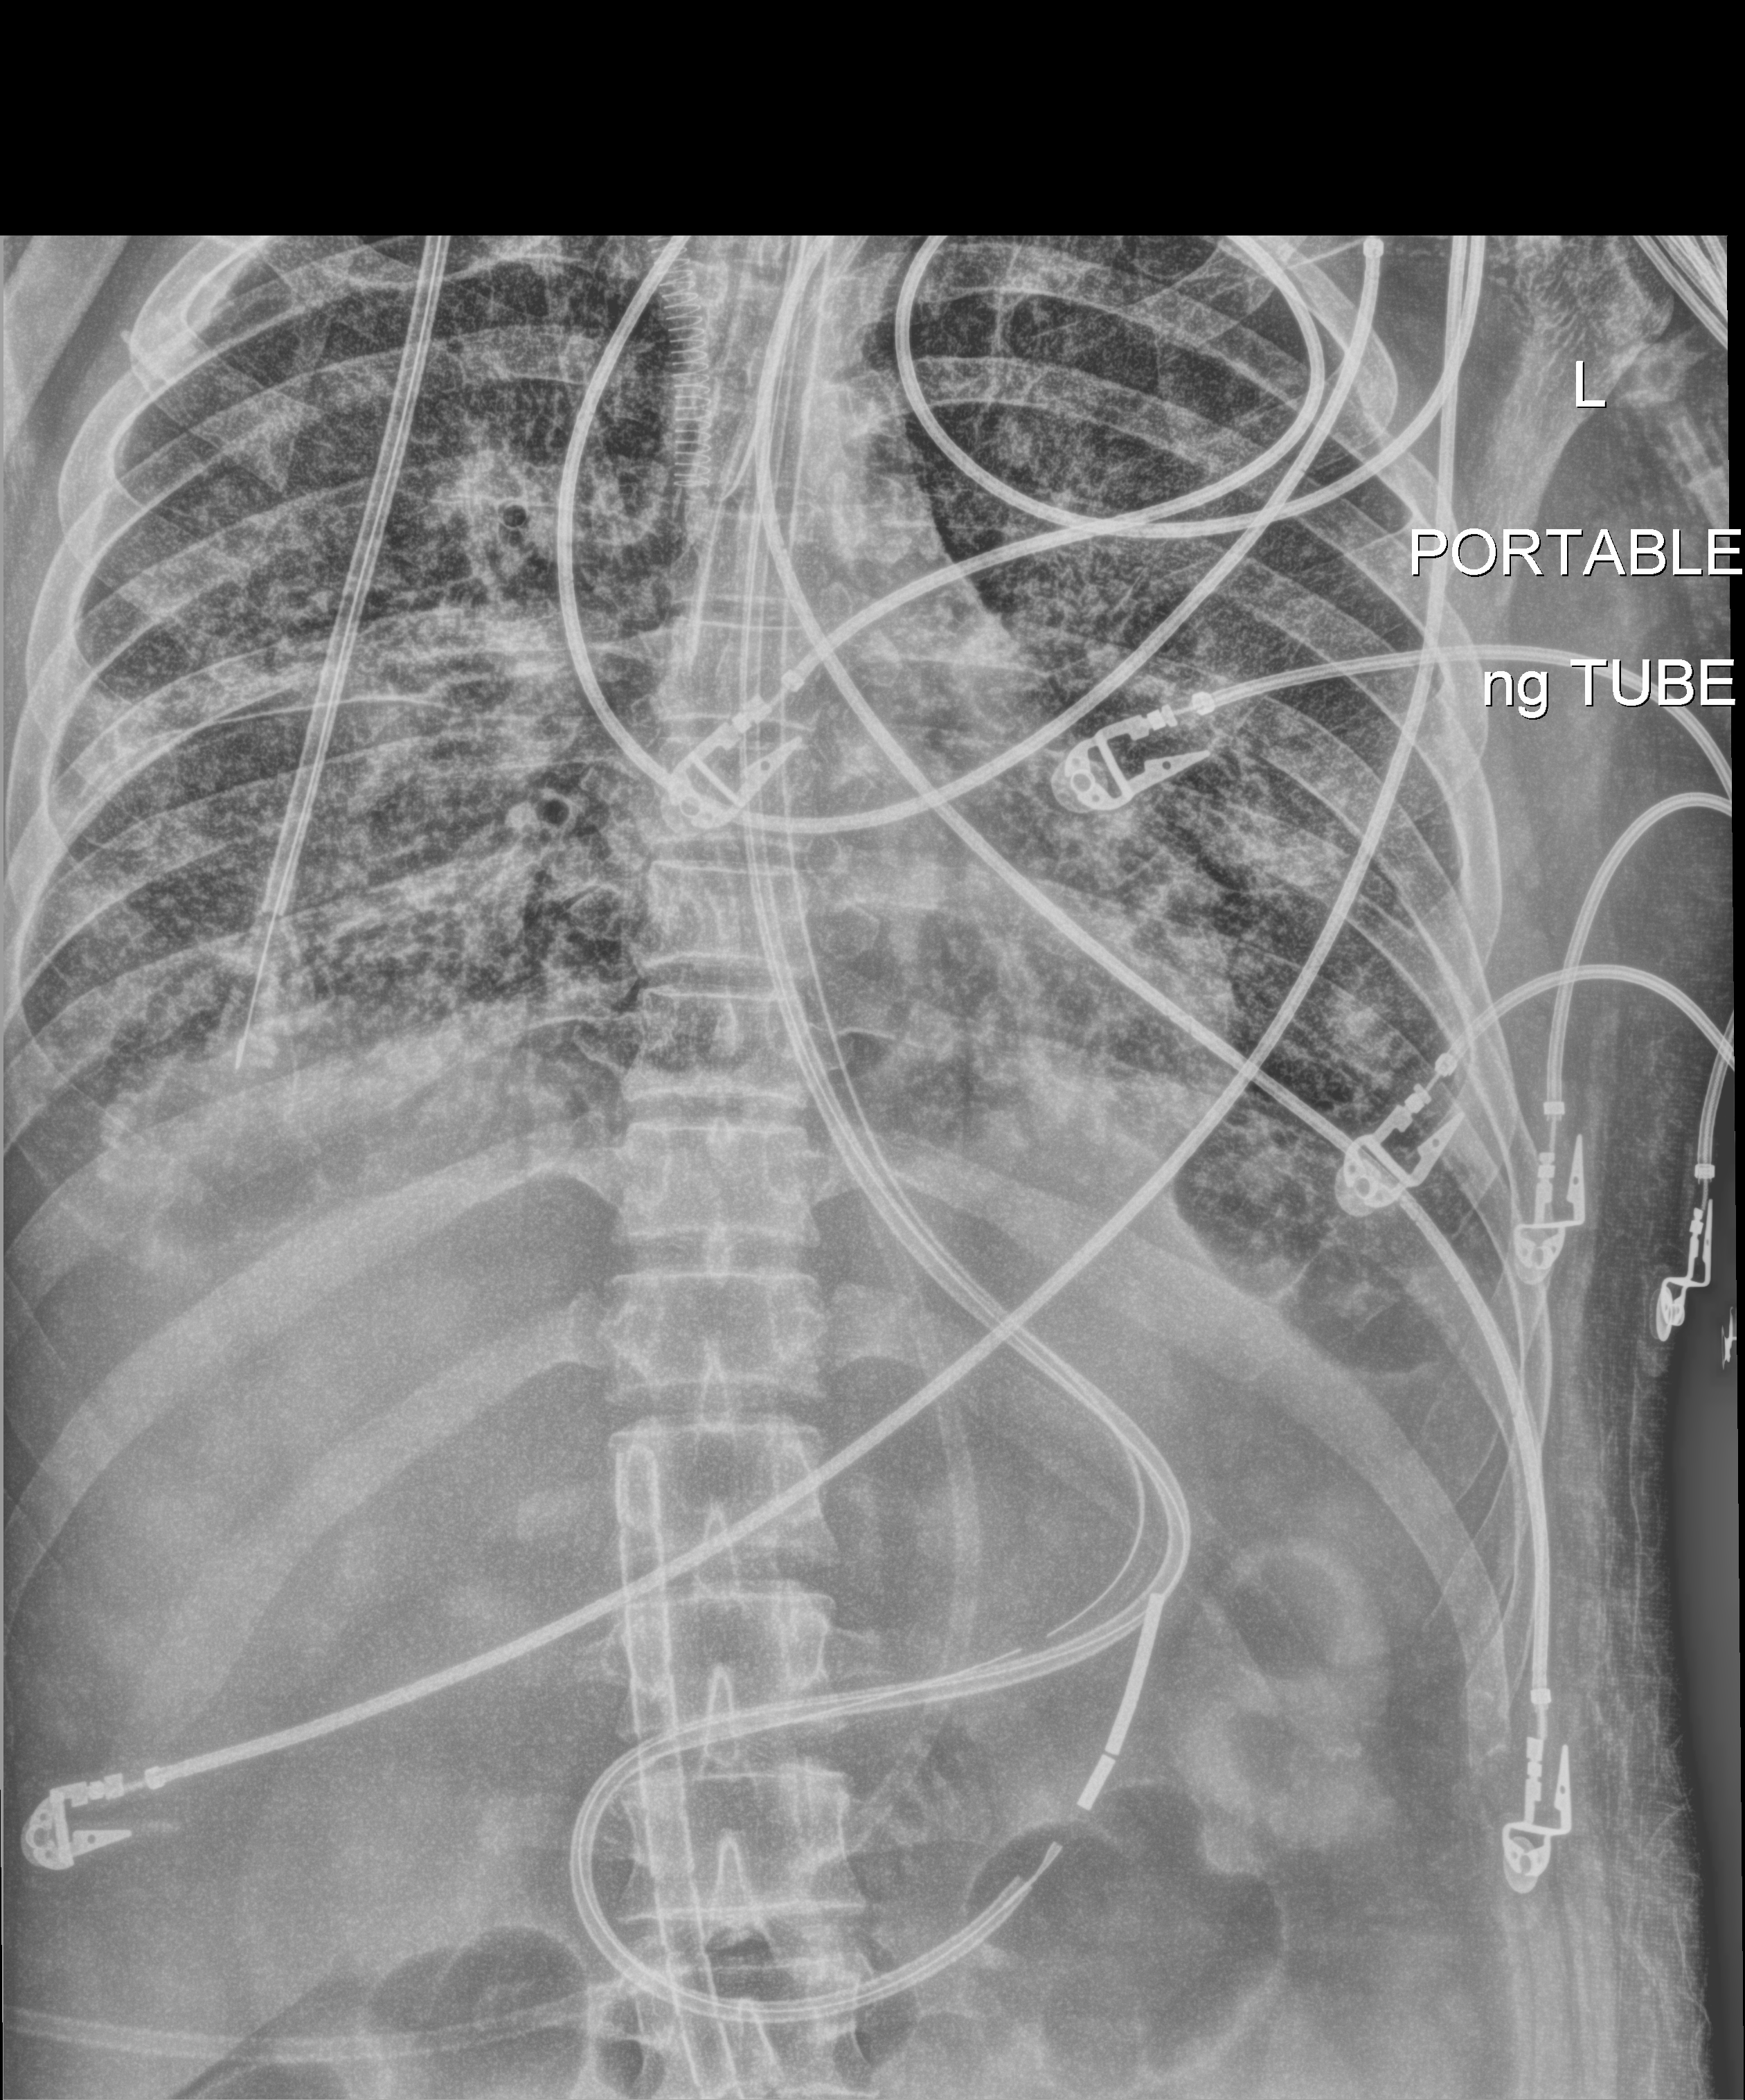
Portable abdomen radiograph; anteroposterior (AP) projection. Patient hospitalised with COVID-19, aged 18–59 years.
Admission-level facts for this patient (not findings on this image; timing relative to this image not recorded): smoking status (admission record): never; admitted to intensive care during this hospital stay: yes; mechanically ventilated during this hospital stay: yes.